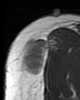
MRI of an extremity soft-tissue mass, one axial slice; position 31 of 46 along the scan axis; MR volume resampled by the dataset authors to the PET/CT grid (not the native acquisition matrix); 80 × 100 image matrix, field of view 78 × 98 mm. Female patient. Case-level facts recorded for this patient, not image findings: histological type: synovial sarcoma; grade: intermediate; site of the primary tumour: right thigh.
Structures marked on this image (expert contour drawn on MRI and transferred to this co-registered scan by the dataset authors):
- gross tumour volume including surrounding oedema: box from (x=21, y=37) to (x=52, y=77) px
- gross tumour volume (mass): (x=21, y=40)–(x=47, y=77)